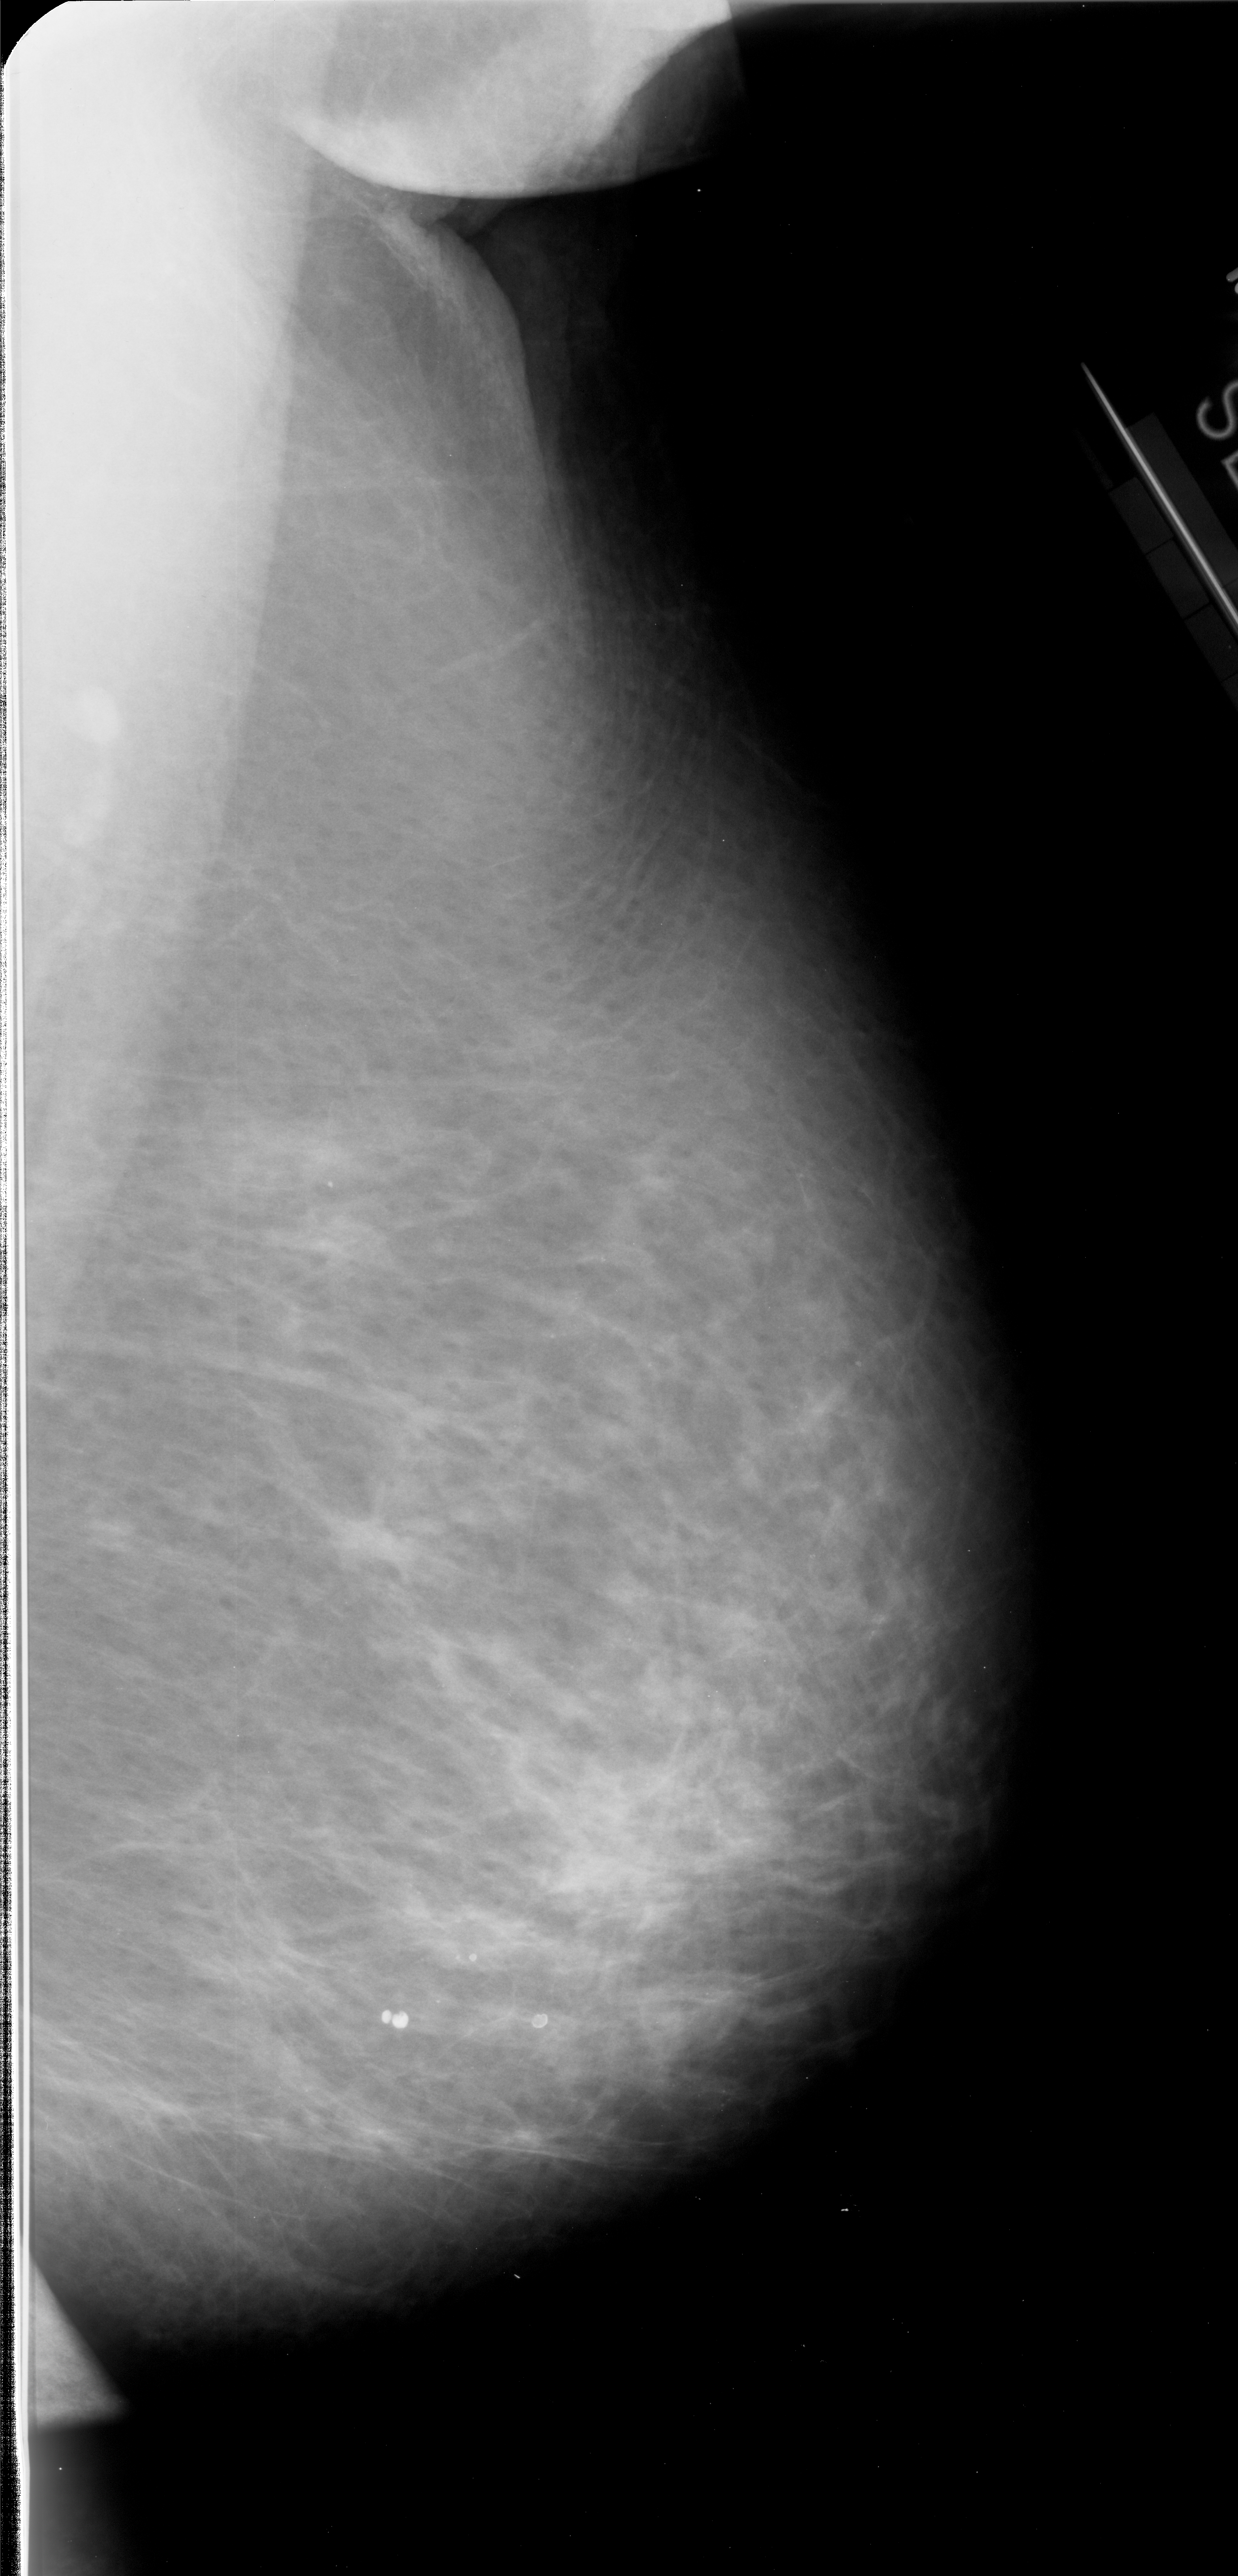
Mammogram (digitized film); right breast; MLO view; BI-RADS breast density category 2 (scale 1–4); 1238 × 2576 image matrix.
Expert-marked regions of interest on this film, with their recorded descriptors:
- mass, shape irregular, margins spiculated; BI-RADS assessment category 4; subtlety rating 1 on a 1 (subtle) to 5 (obvious) scale; pathology (as recorded): malignant: box from (x=316, y=1485) to (x=427, y=1582) px